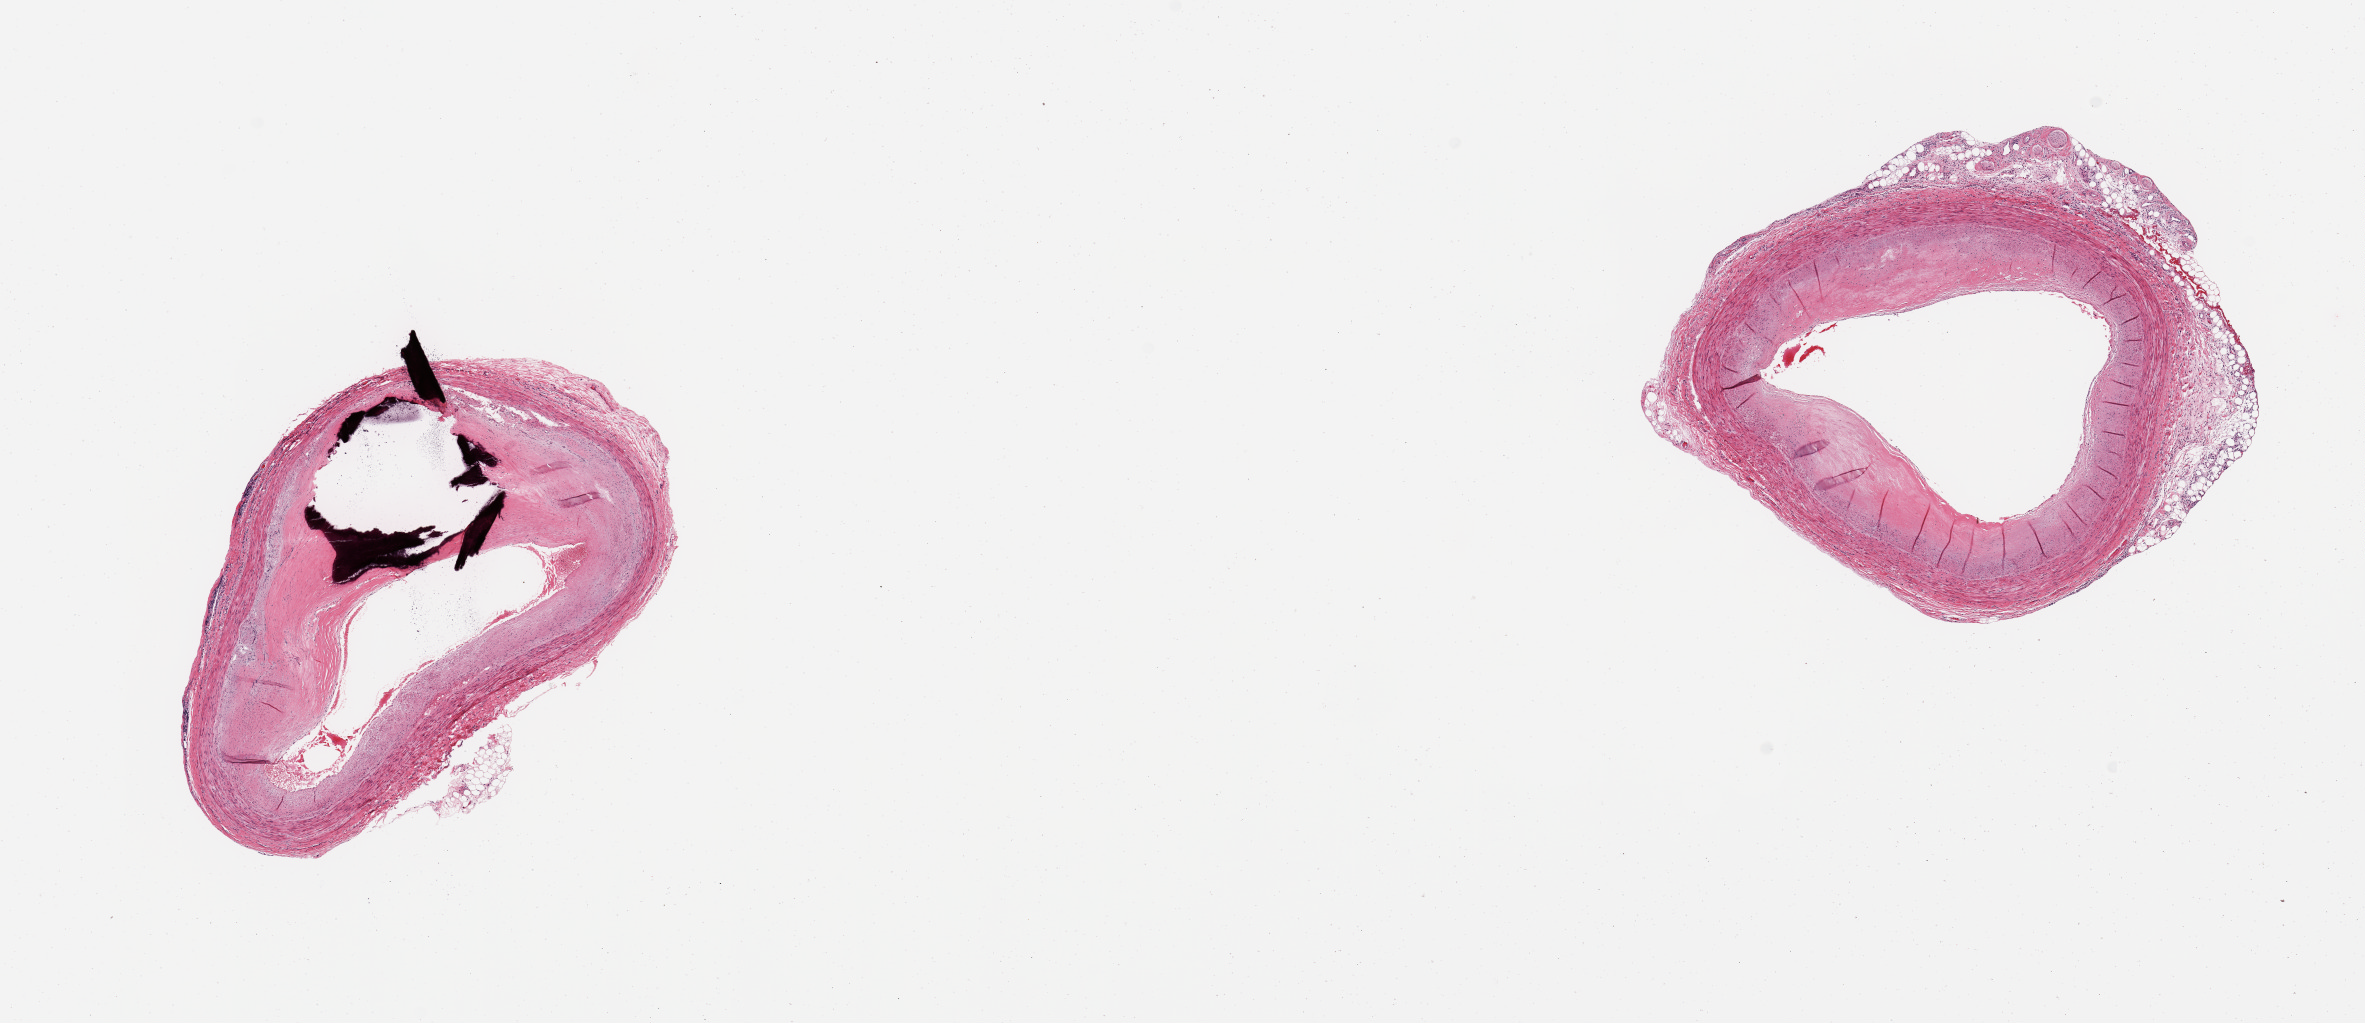
Whole-slide image, hematoxylin and eosin (H&E) stain, a low-resolution overview of the entire scanned area, about 18.7 x 8.1 mm; PAXgene-fixed paraffin-embedded (PFPE) section; target tissue: coronary artery; donor tissue sample.
Reviewer comment on this tissue sample: 2 pieces; moderate plaque with large calcific deposit in 1.